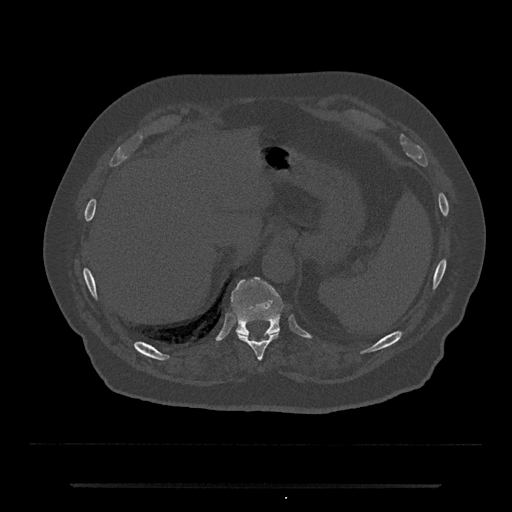
CT including the spine, one axial slice. Position 680 of 797 along the scan axis. Bone window (W 1800 / L 400 HU). 0.5 mm slice thickness. 512 × 512 image matrix, field of view 434 × 434 mm. Patient: male, 80 years. Case-level facts recorded for this patient, not image findings: primary cancer: prostate; vertebrae with lytic lesions (as recorded): L1, T11.
Outlined on this slice (semi-automatic segmentation, software-assisted and operator-edited):
- T10 vertebra: box from (x=237, y=332) to (x=279, y=361) px
- T11 vertebra: (x=231, y=277)–(x=284, y=336)